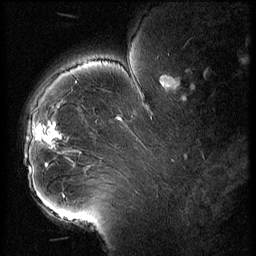
Breast MRI (dynamic contrast-enhanced), one sagittal slice; slice 43 of 56 in the series (ordered by position); 3 images stored at this slice position (order not interpretable as contrast timing); 1.5 T; TE 4.2 ms, TR 9 ms; 2.5 mm slice thickness; 256 × 256 image matrix, field of view 180 × 180 mm. Female patient, age 43 years. From the clinical record (not read from this slice): setting: breast cancer imaged before/during neoadjuvant chemotherapy; receptor status: HER2-positive.
Structures marked on this image (semi-automatically segmented with operator editing):
- analysis volume of interest (the breast-tissue region the enhancement analysis was run in; not a lesion): box from (x=24, y=92) to (x=74, y=211) px
- tumour enhancement mask (voxels above the 140 % enhancement threshold inside the analysis volume of interest): (x=37, y=126)–(x=62, y=143)